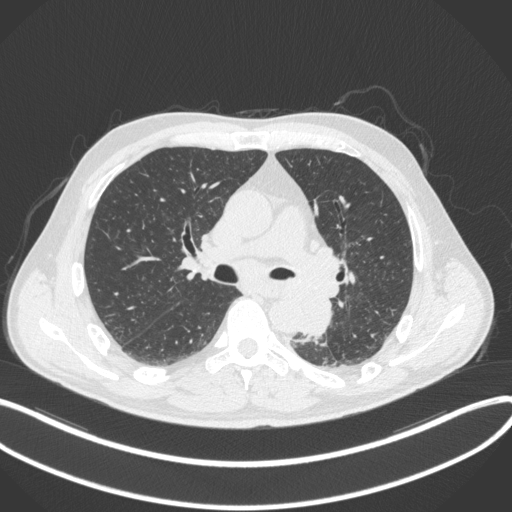
Chest CT, one axial slice. Position 206 of 328 along the scan axis. 120 kVp. Lung window (W 1500 / L -600 HU). 1 mm slice thickness. 512 × 512 image matrix. Patient: male, 59 years. From the clinical record (not read from this slice): clinical TNM (as recorded): T2a N2 M0.
Structures marked on this image (rectangle marked by the reading radiologist):
- lung tumour (recorded histology: squamous cell carcinoma): bounding box [x1, y1, x2, y2] px = [300, 287, 336, 340]